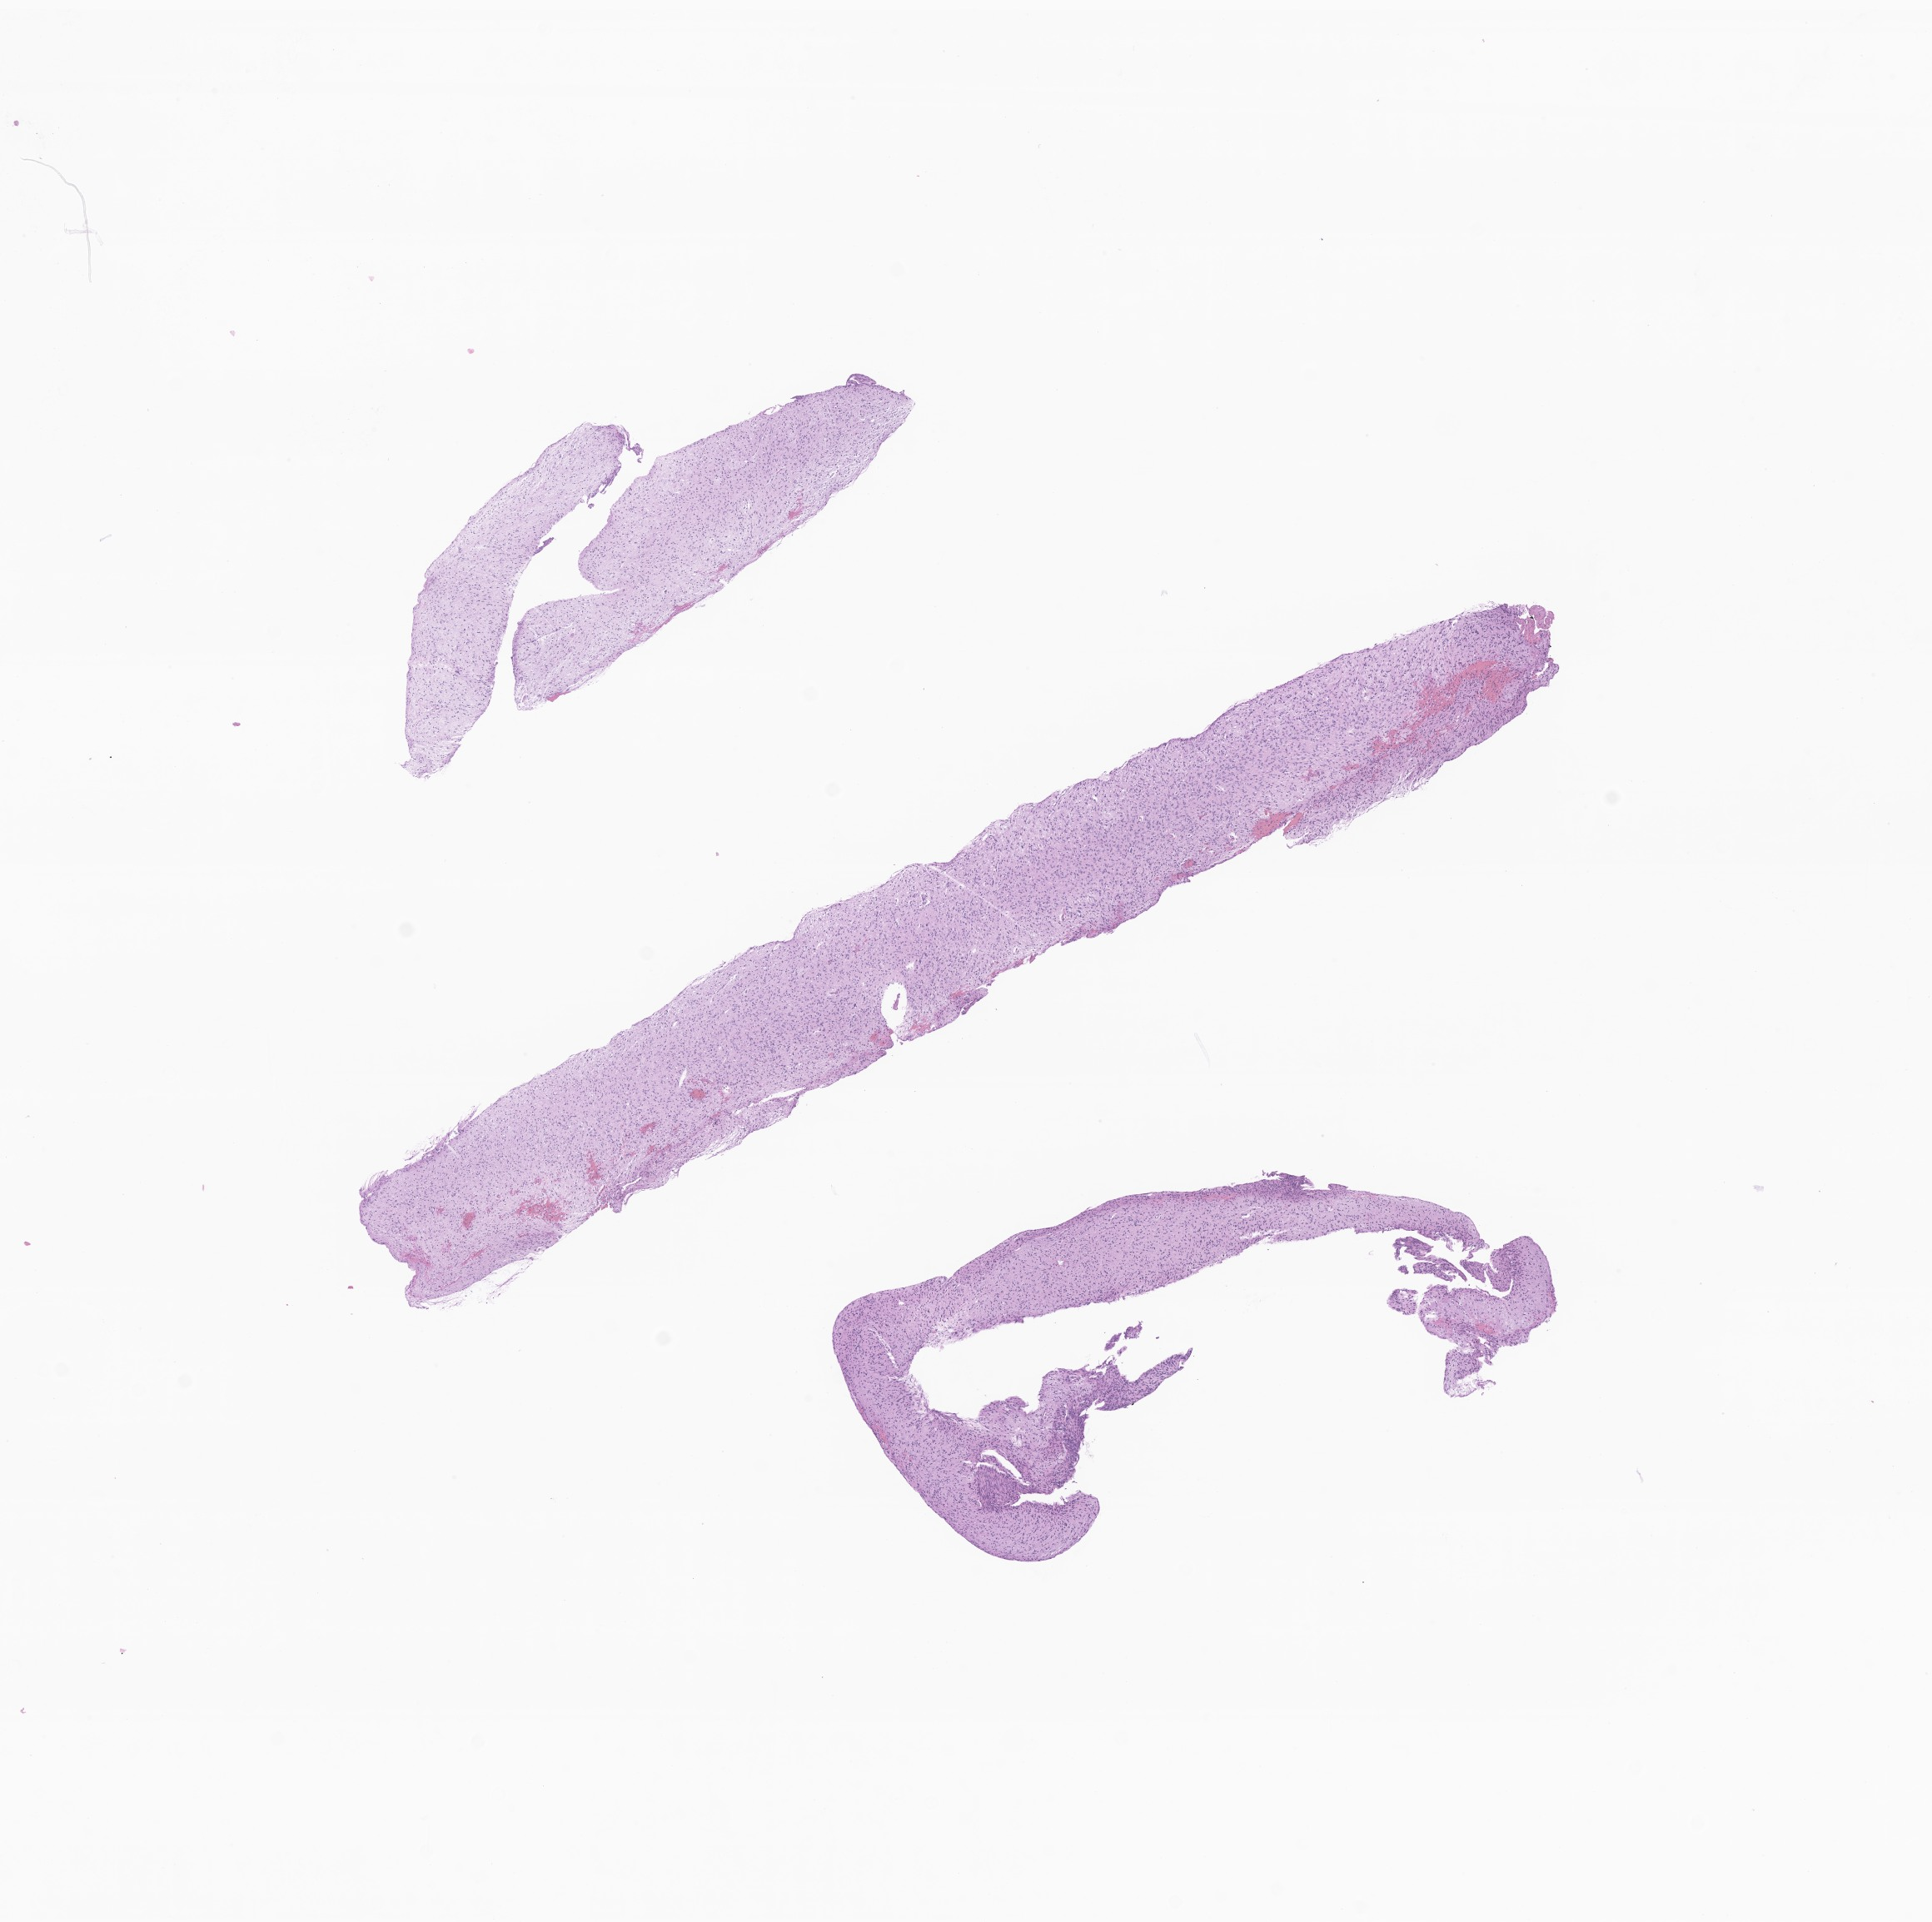
Digitized H&E-stained section of tumor tissue from the cerebrum, whole scanned area (about 9.8 x 9.7 mm) shown as a low-resolution overview, FFPE section. Patient: female, age 68 months (5 years 8 months).
- diagnosis (ICD-O-3 morphology term): Glioma, malignant